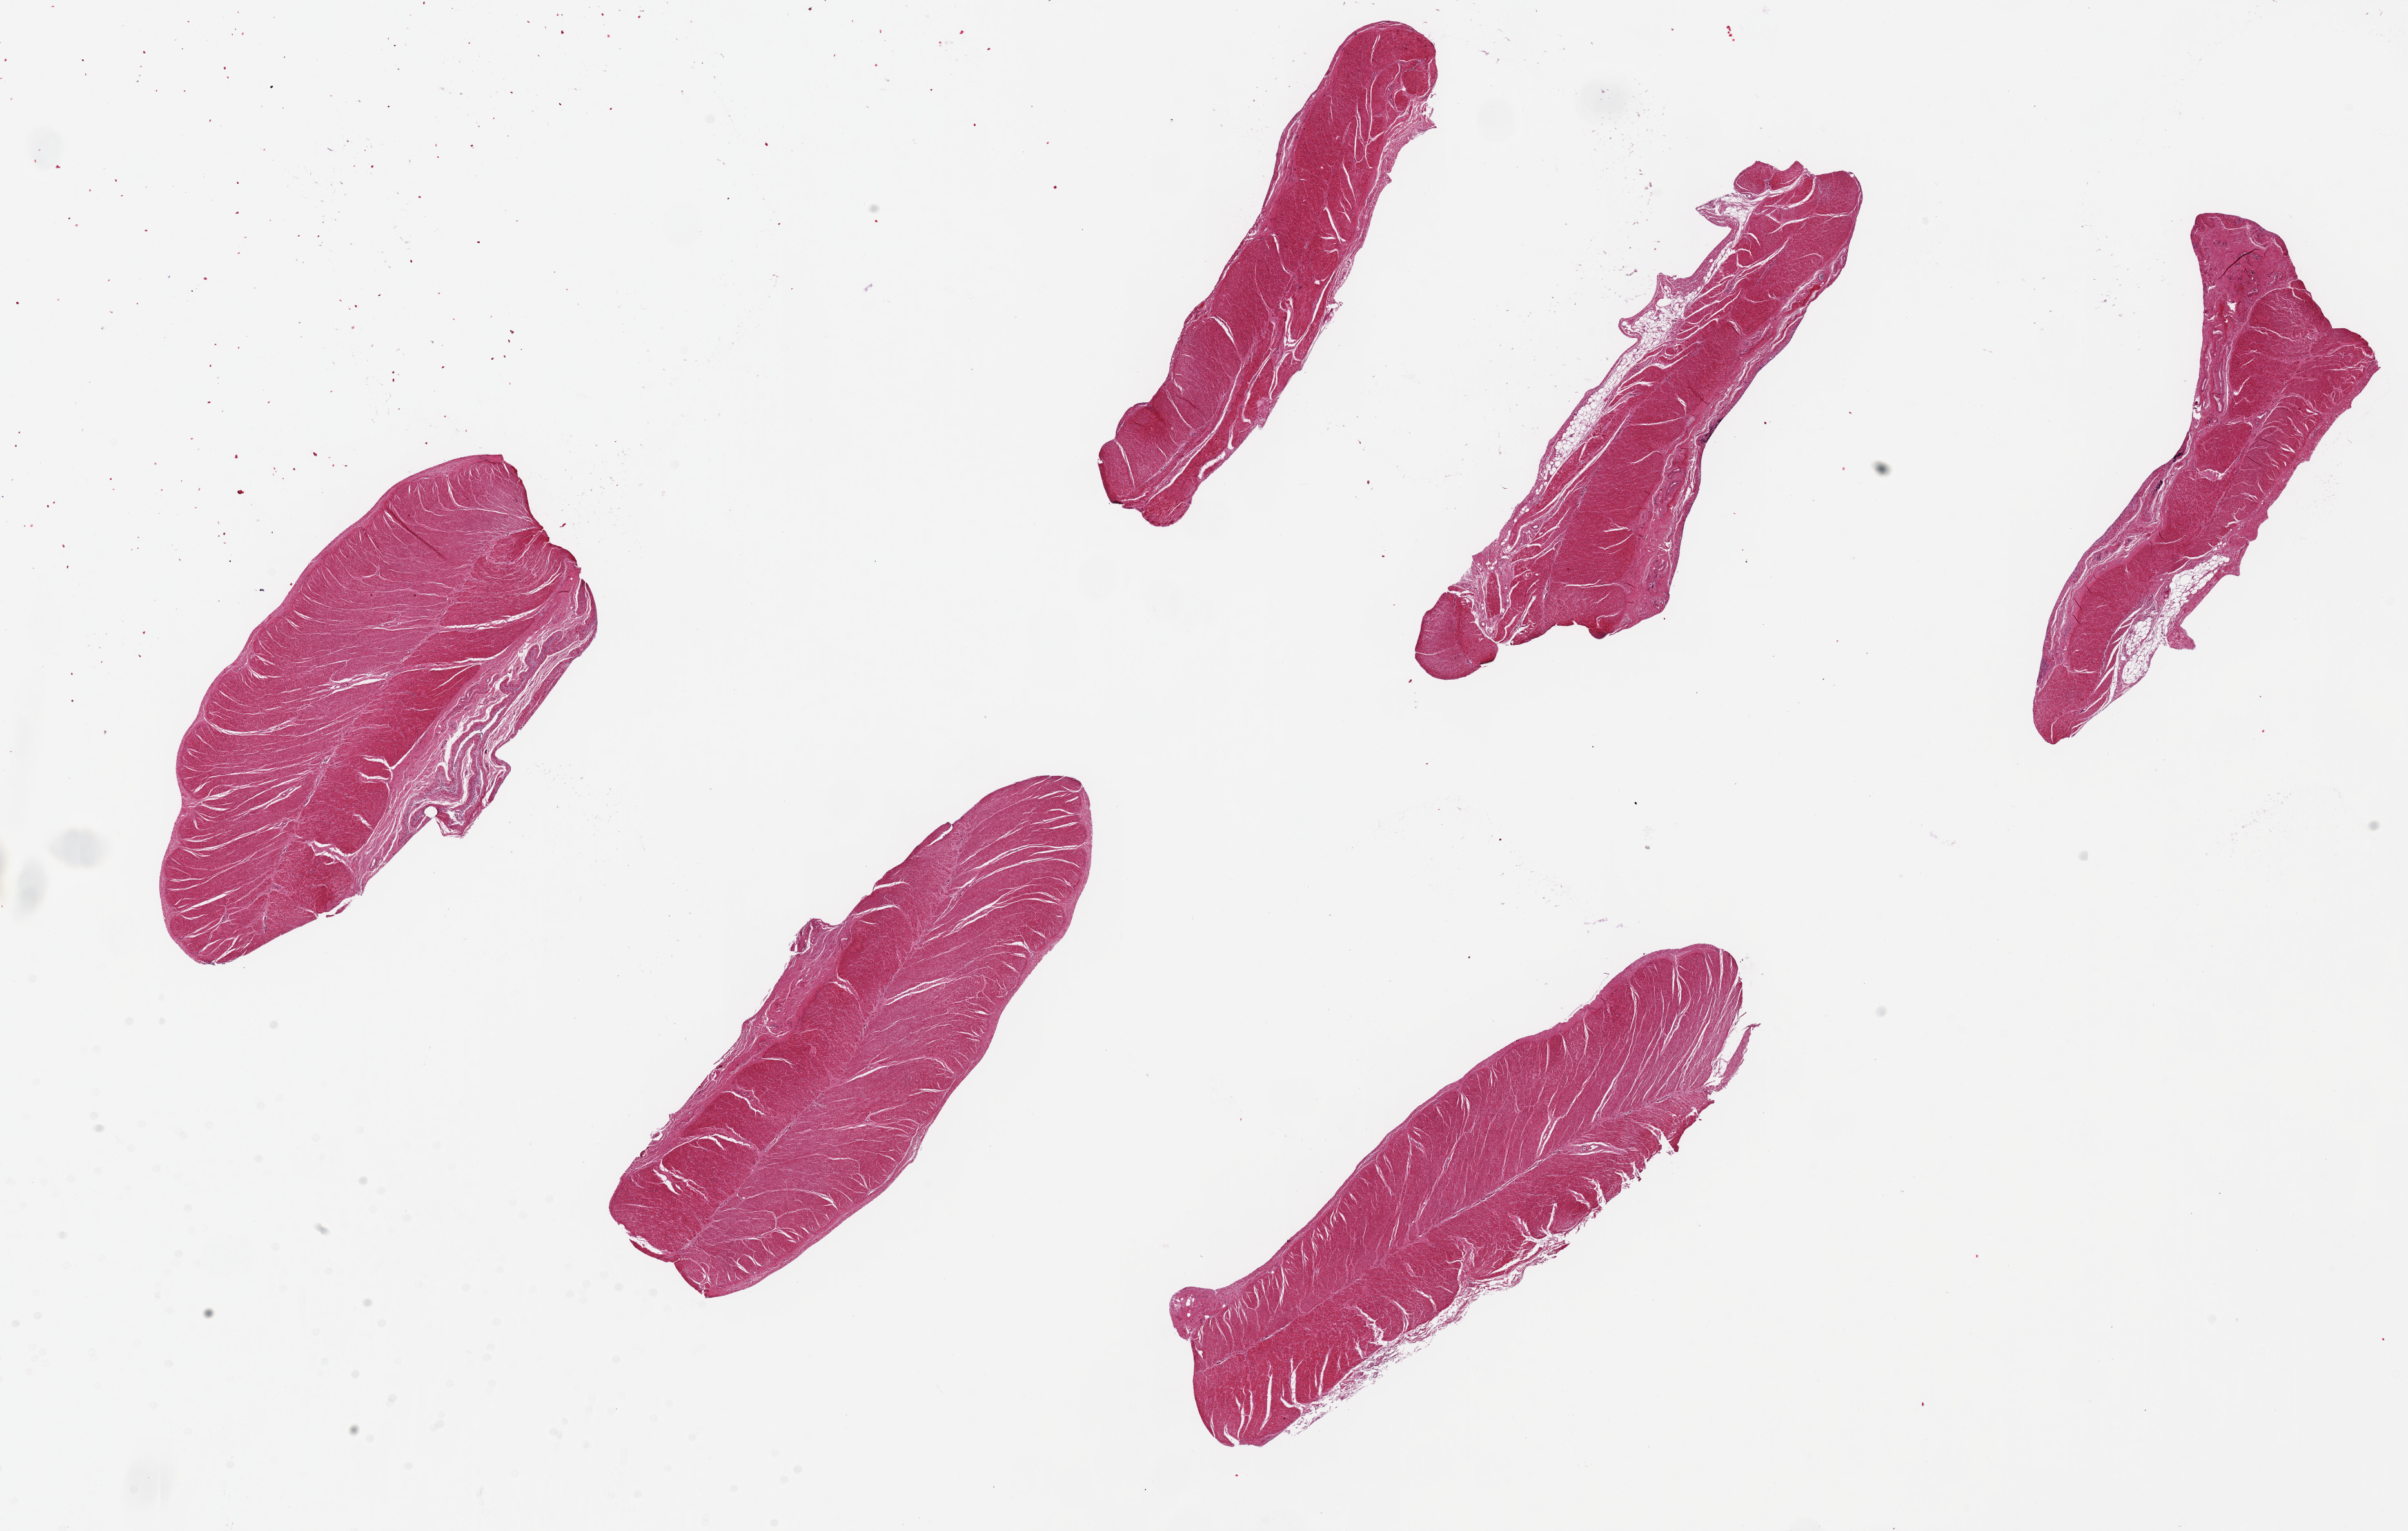
Digitized hematoxylin and eosin (H&E)-stained section, a low-resolution overview of the entire scanned area, about 29.5 x 18.8 mm (from a 20x scan). PAXgene-fixed paraffin-embedded (PFPE) section. Target tissue: sigmoid colon. Tissue donor sample. Donor: male.
Reviewer comment on this tissue sample: 6 pieces, up to 9x2mm; Well trimmed muscle. 10% subserosal adipose on 2 pieces.